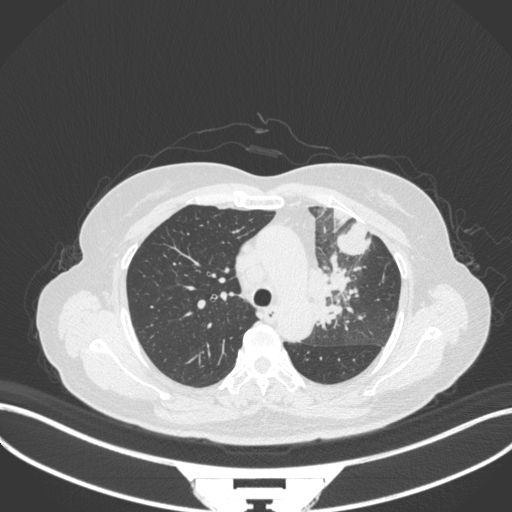
Chest CT, one axial slice; slice 238 of 382 in the series (ordered by position); reconstruction kernel B31f; lung window (W 1500 / L -600 HU); 512 × 512 image matrix. Female patient, age 64 years. Case-level facts recorded for this patient, not image findings: clinical TNM (as recorded): T2a N2 M0.
Outlined on this slice (bounding box drawn by a radiologist):
- lung tumour (recorded histology: adenocarcinoma): bounding box <308,256,362,335> (left, top, right, bottom; pixels)
- lung tumour (recorded histology: adenocarcinoma): <333,218,372,257>